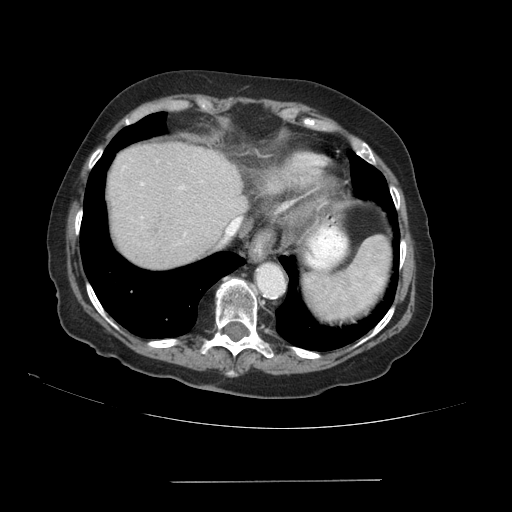
Contrast-enhanced abdominal CT (liver protocol), one axial slice; position 76 of 89 along the scan axis; reconstruction kernel STANDARD; soft-tissue window (W 400 / L 40 HU); 2.5 mm slice thickness; 512 × 512 image matrix. Case-level facts recorded for this patient, not image findings: diagnosis: hepatocellular carcinoma (patient treated with transarterial chemoembolisation; whether this scan precedes or follows treatment is not stated here); TNM stage (as recorded): Stage-IVA; Child-Pugh class: A; tumour nodularity: uninodular.
Annotated regions visible in this slice (semi-automatic segmentation, software-assisted and operator-edited):
- liver parenchyma outside the tumour (the mass and vessels are separate outlines, so this box may not span the whole liver): bounding box <106,142,246,268> (left, top, right, bottom; pixels)
- liver vessels: <141,183,184,189>